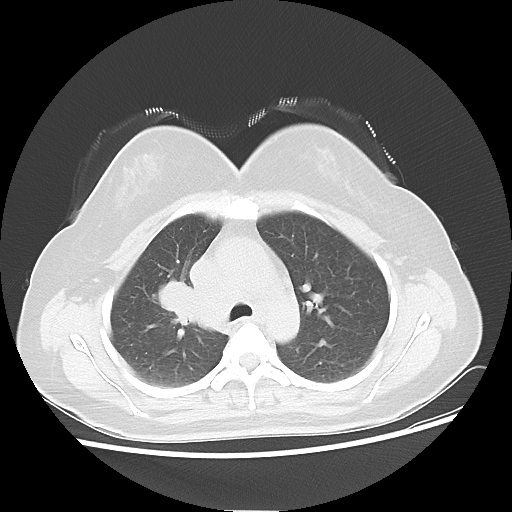
Chest CT, one axial slice. Position 35 of 50 along the scan axis. Reconstruction kernel LUNG. 100 kVp. Lung window (W 1500 / L -600 HU). 512 × 512 image matrix, field of view 360 × 360 mm. Patient: female, 40 years. Case-level facts recorded for this patient, not image findings: clinical TNM (as recorded): T1c N3 M0.
Annotated regions visible in this slice (rectangle marked by the reading radiologist):
- lung tumour (recorded histology: small cell carcinoma): bounding box [x1, y1, x2, y2] px = [154, 271, 195, 319]